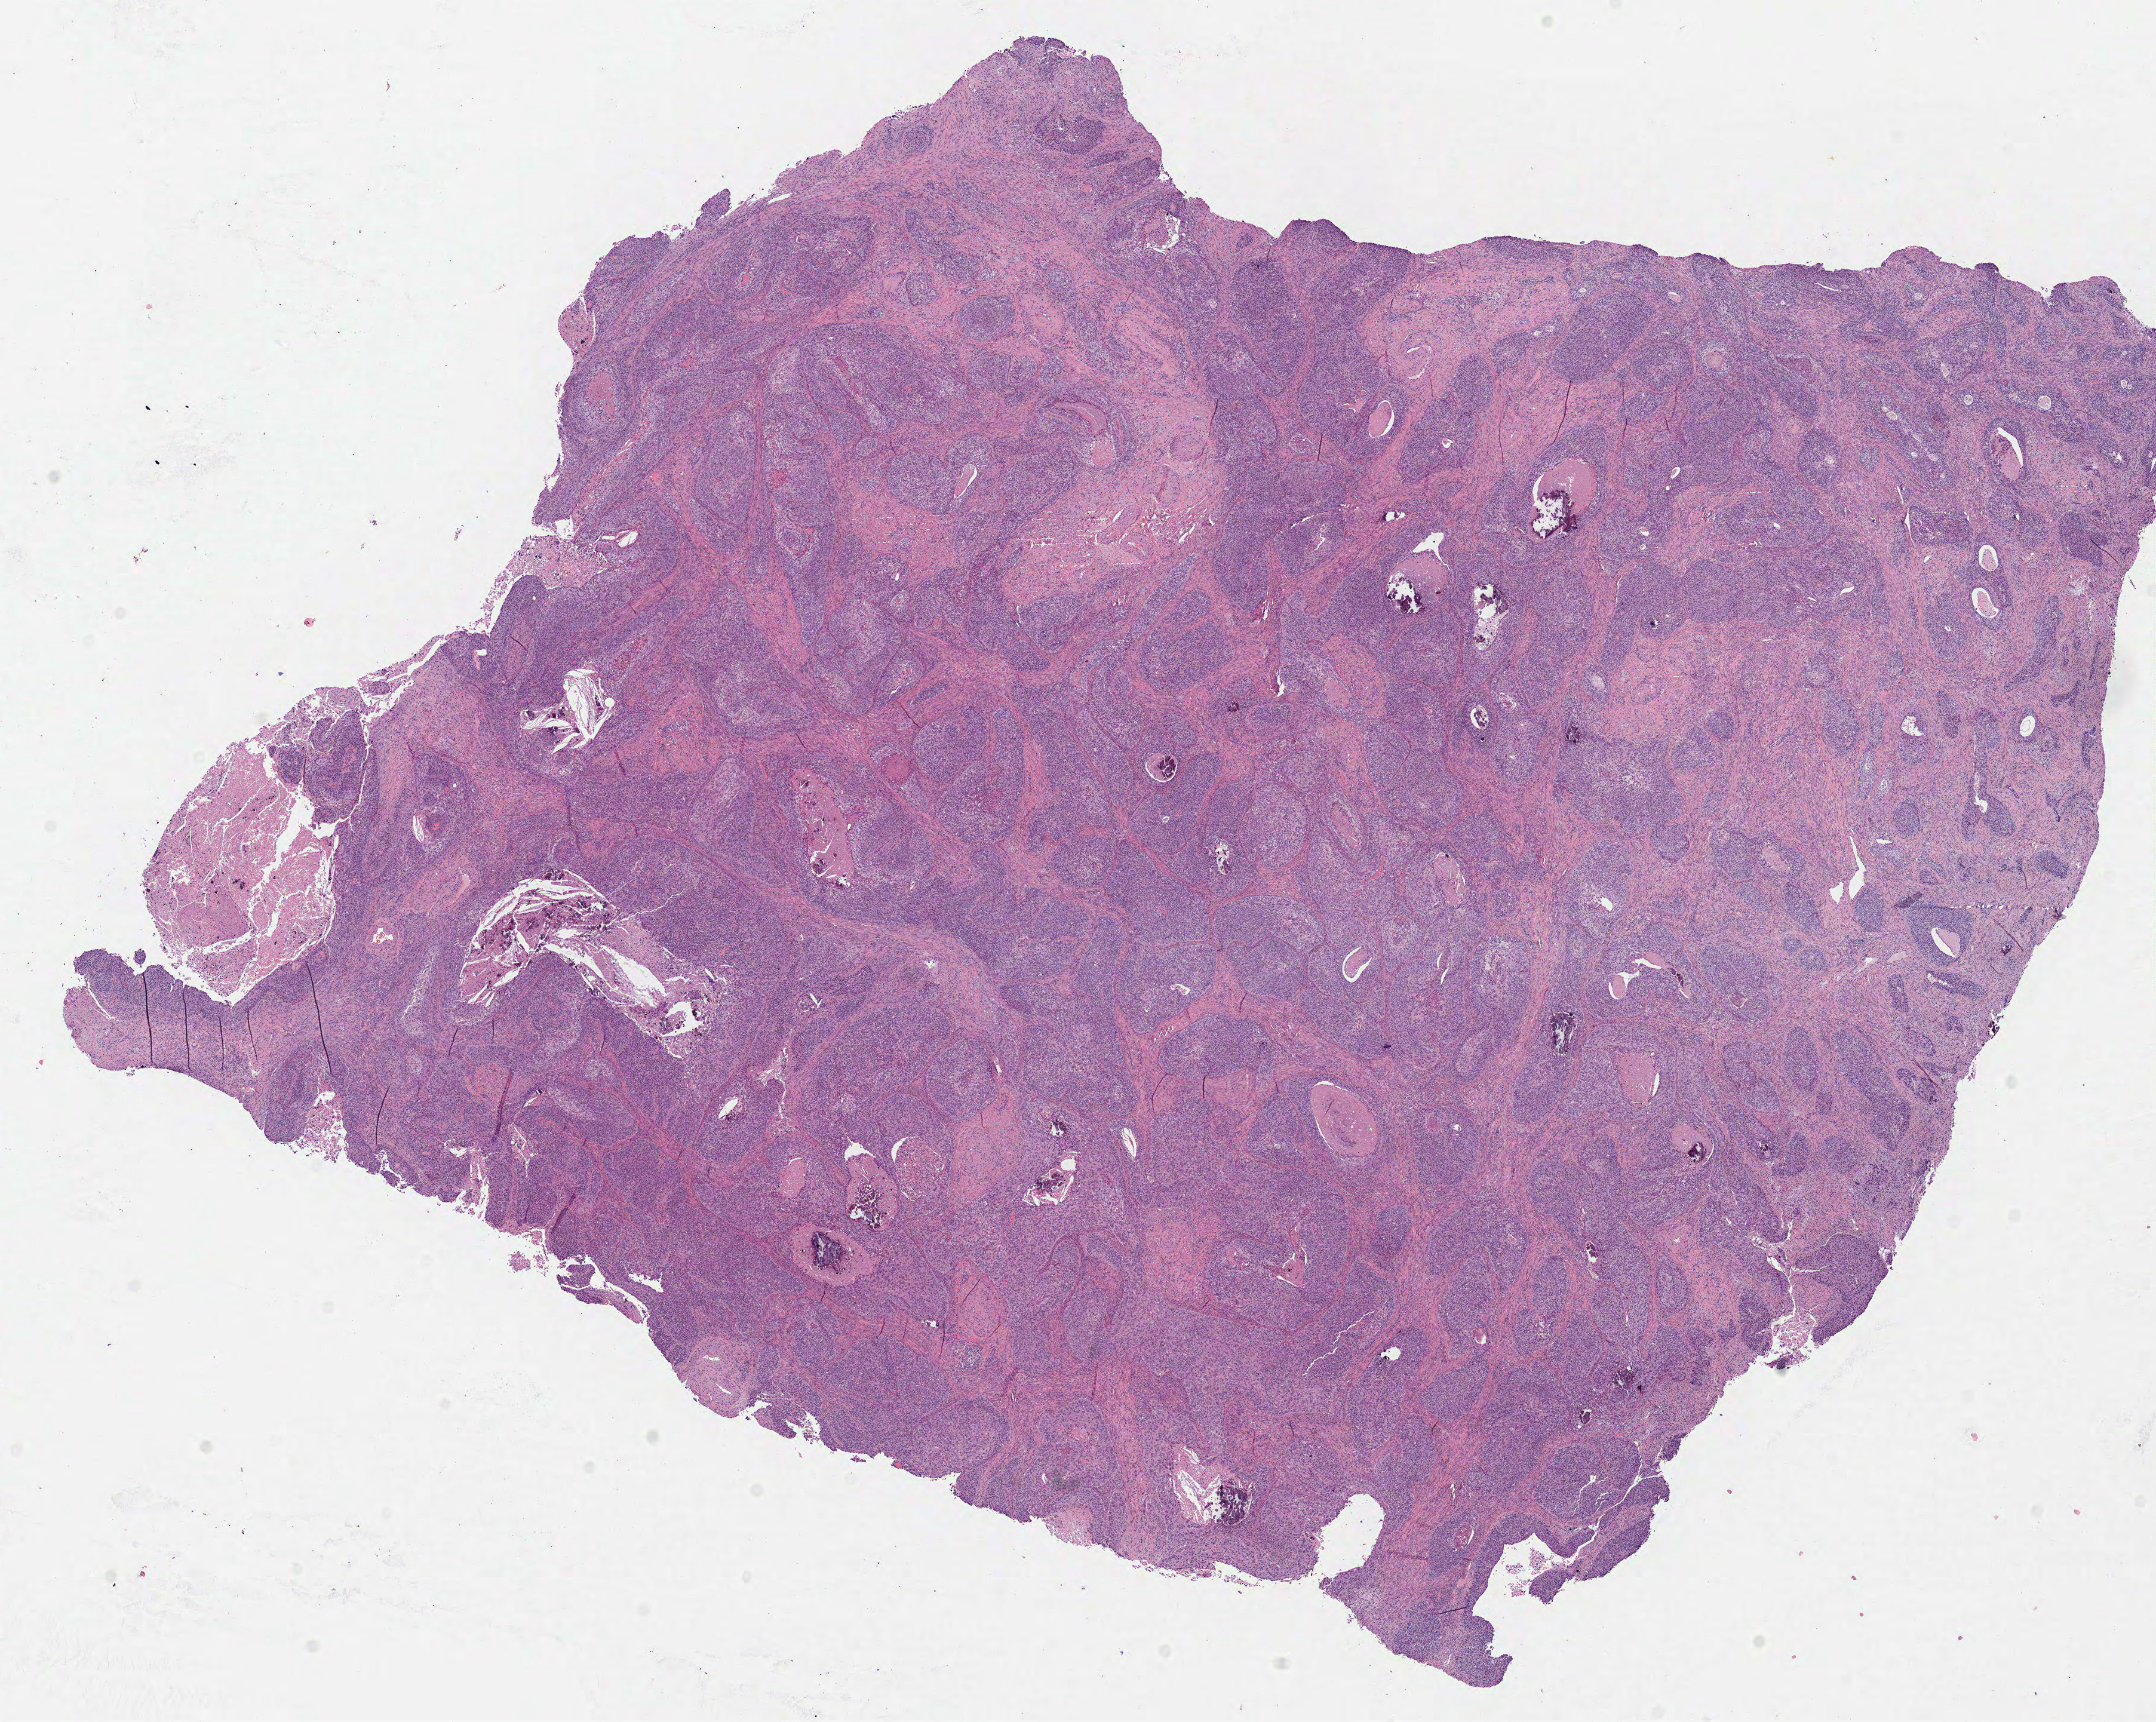
H&E-stained whole-slide image, a low-resolution overview of the entire scanned area, about 14.2 x 11.3 mm (from a 40x scan). FFPE section. Cervix, primary tumour sample. Female, age 60 years at initial diagnosis. Histologic grade: G3 (poorly differentiated).
- diagnosis: Squamous cell carcinoma, NOS (cervix uteri)
- FIGO stage: IIA1